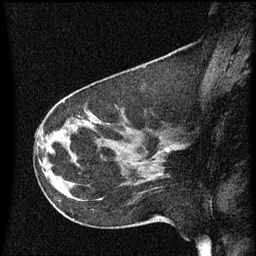
Breast MRI (dynamic contrast-enhanced), one sagittal slice; position 27 of 60 along the scan axis; dynamic contrast-enhanced series, image 2 of 3 at this slice position (ordered by acquisition); 1.5 T; TE 4.2 ms, TR 8.4 ms; 256 × 256 image matrix, field of view 200 × 200 mm. Female patient, age 41 years. From the clinical record (not read from this slice): setting: breast cancer imaged before/during neoadjuvant chemotherapy; receptor status: triple-negative.
Outlined on this slice (semi-automatically segmented with operator editing):
- analysis volume of interest (the breast-tissue region the enhancement analysis was run in; not a lesion): bounding box (x1, y1, x2, y2) in pixels: (133, 122, 188, 175)
- tumour enhancement mask (voxels above the 70 % enhancement threshold inside the analysis volume of interest): (164, 148, 169, 151)